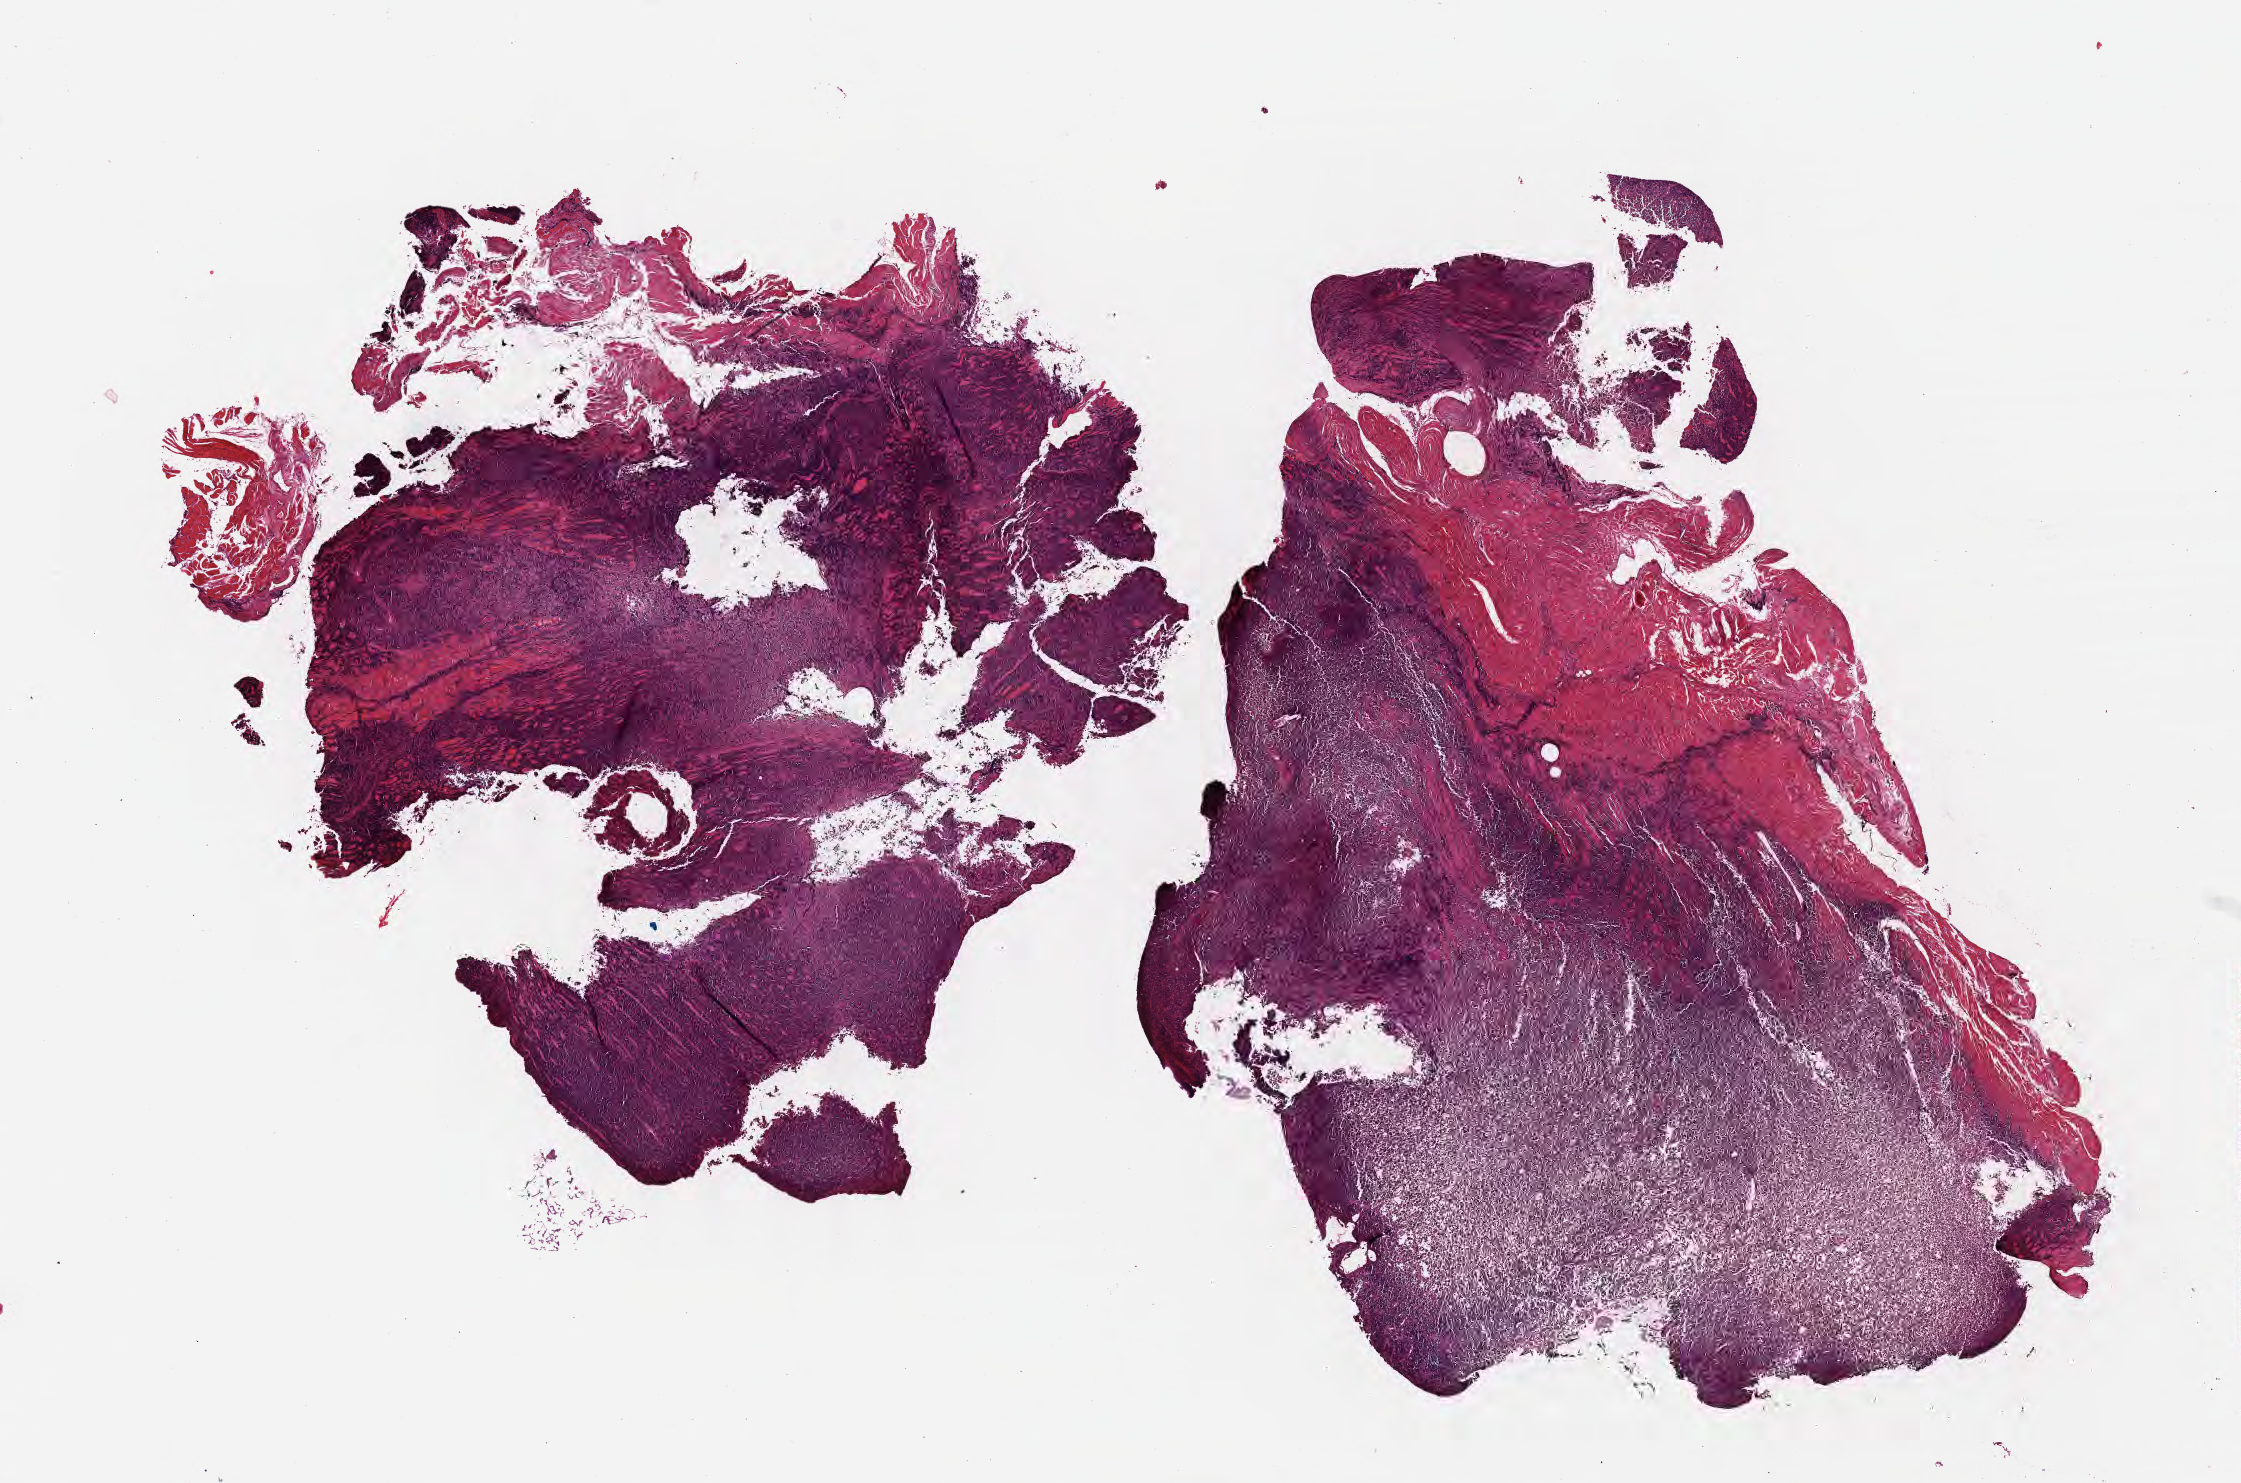
Whole-slide image, hematoxylin and eosin (H&E) stain, shown as a low-resolution overview of the whole scanned area (about 18.1 x 12.0 mm). Formalin-fixed paraffin-embedded section. Specimen: primary tumor. Male patient, aged 40. Slide review estimates, as recorded: tumor cells 90%, tumor nuclei 95%, stromal cells 10%, necrosis 0%, normal cells 0%. Inflammatory infiltration, as recorded: lymphocyte infiltration 50%, monocyte infiltration 15%, neutrophil infiltration 5%.
- Ann Arbor stage (patient): Stage III
- histologic diagnosis: Burkitt lymphoma, NOS